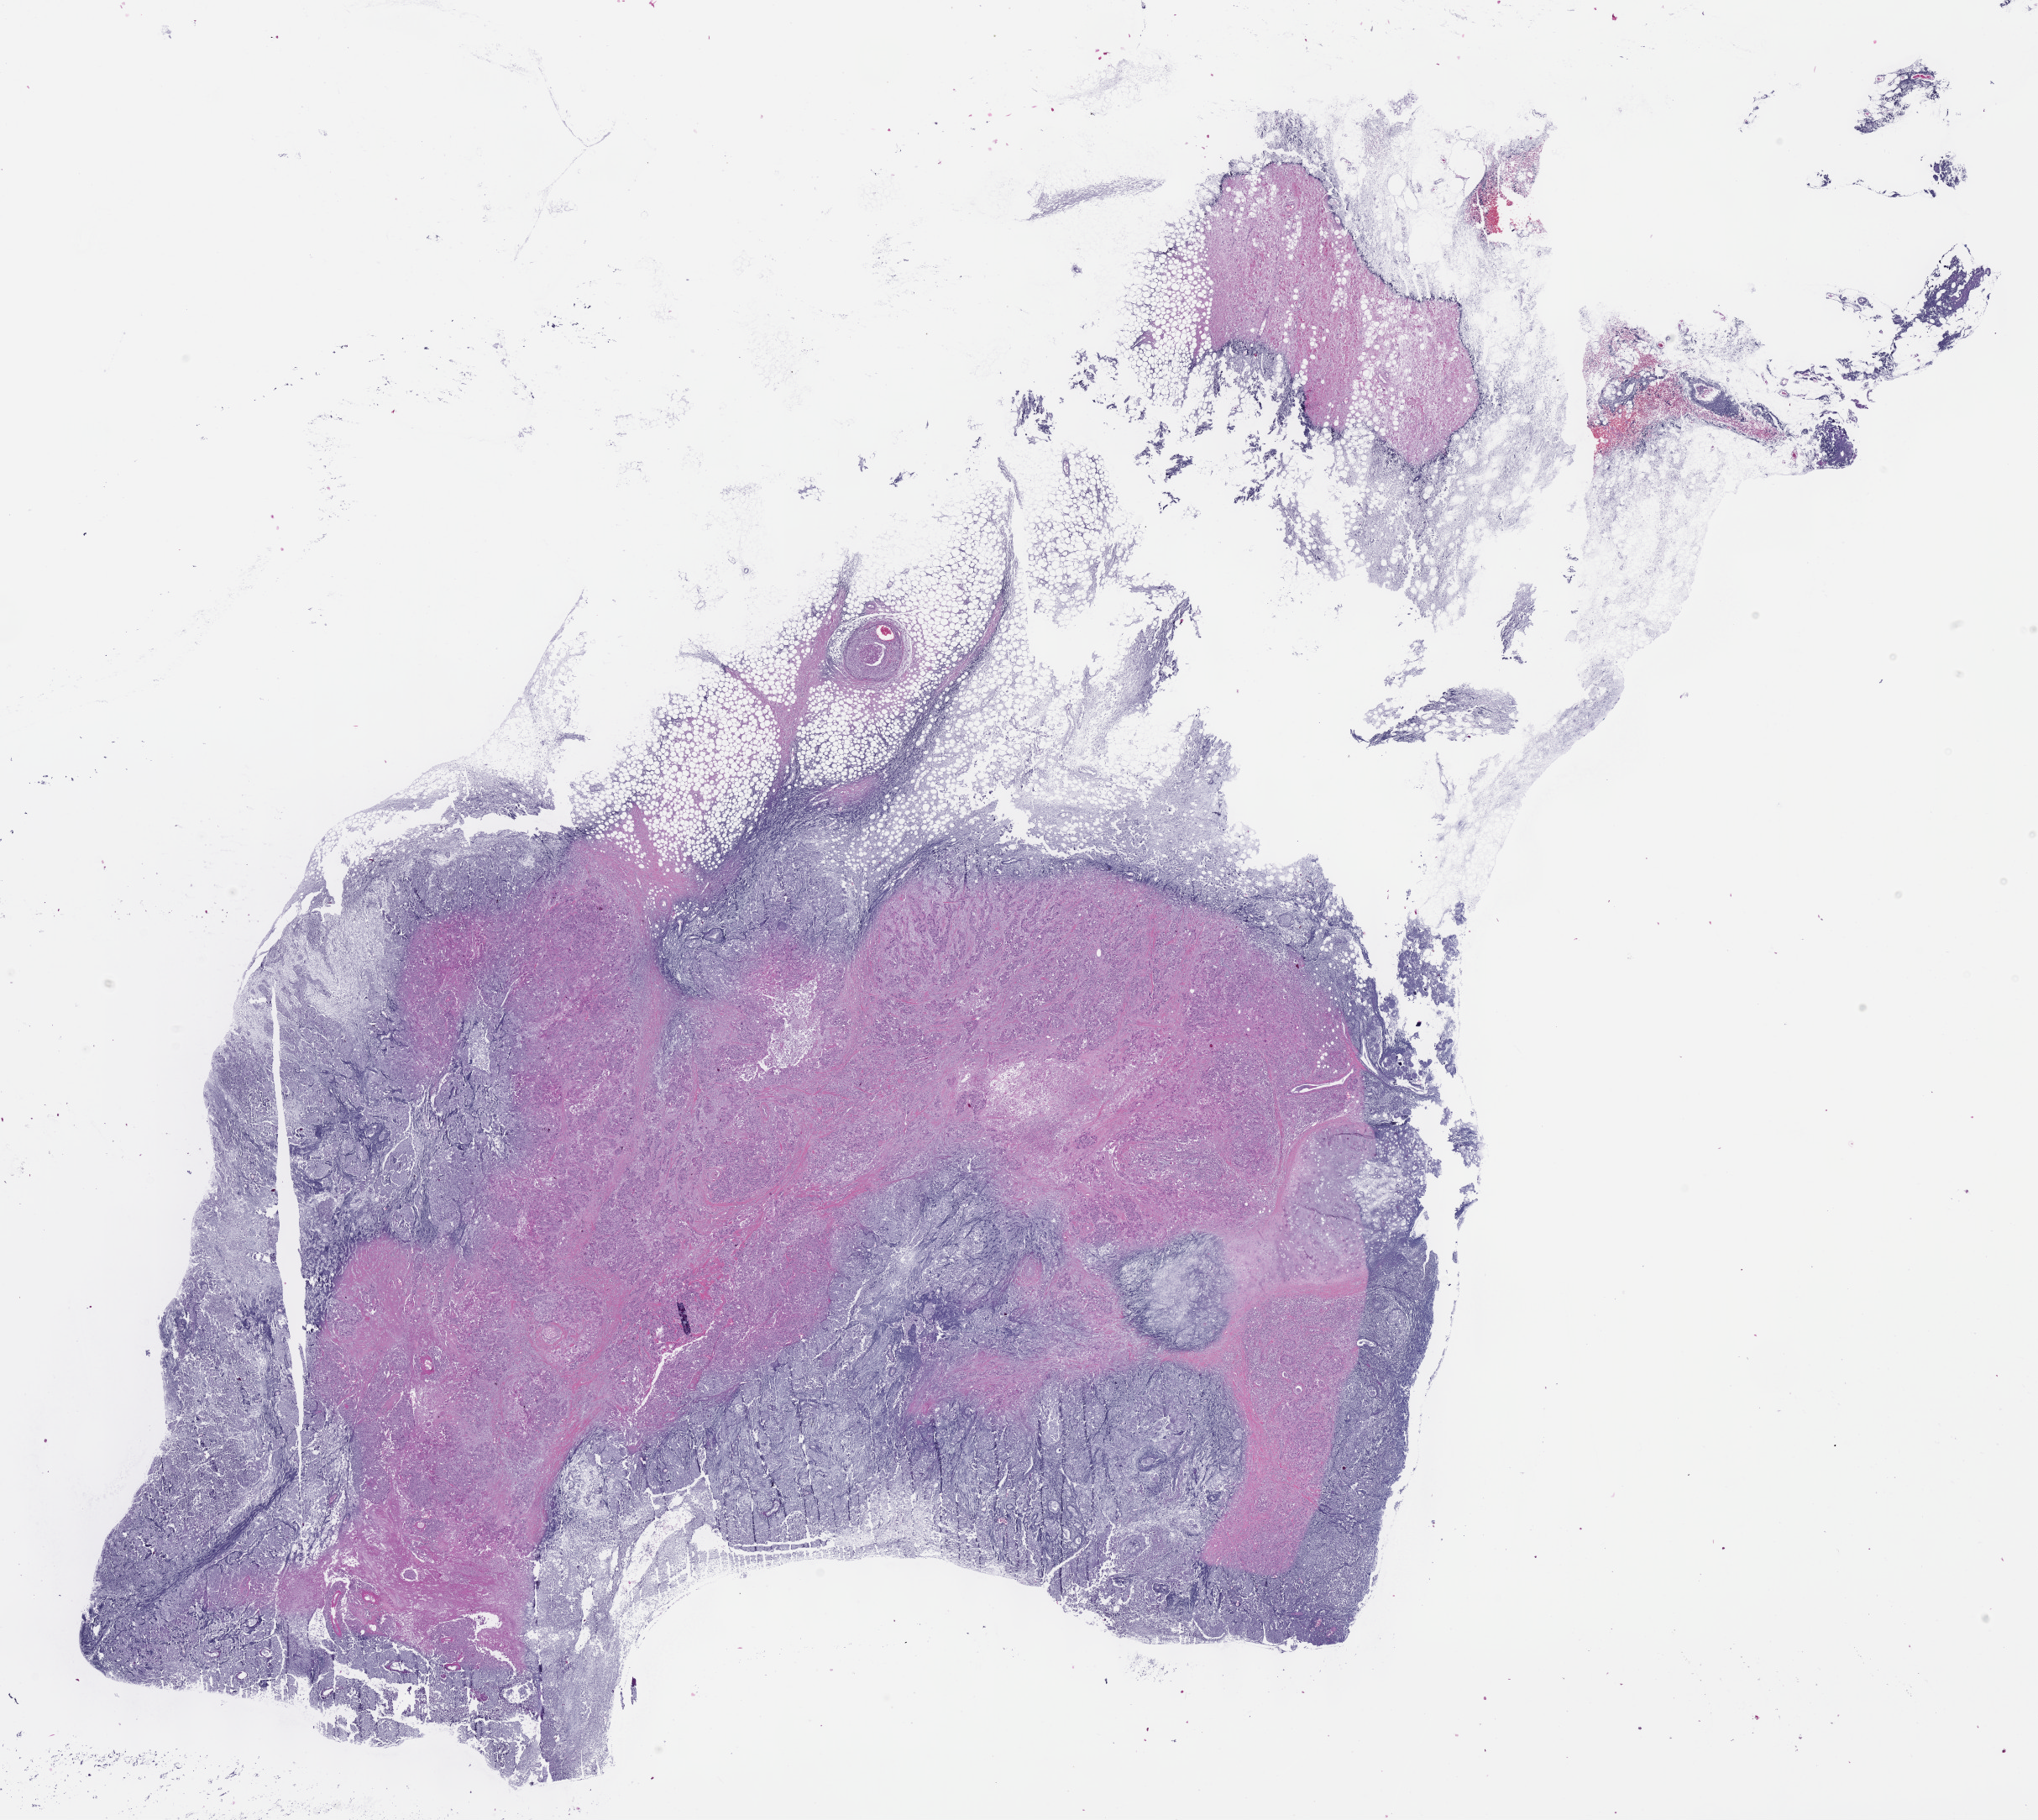
H&E whole-slide image — low-resolution overview of the scanned area, about 19.6 x 17.5 mm (slide scanned at 40x); formalin-fixed paraffin-embedded (FFPE) diagnostic section; sample: primary tumour, head and neck. Male patient; age at initial diagnosis 77 years. Histologic grade: GX (grade cannot be assessed).
AJCC pathologic stage: II (7th edition). Histologic diagnosis: Squamous cell carcinoma, NOS (larynx, NOS).